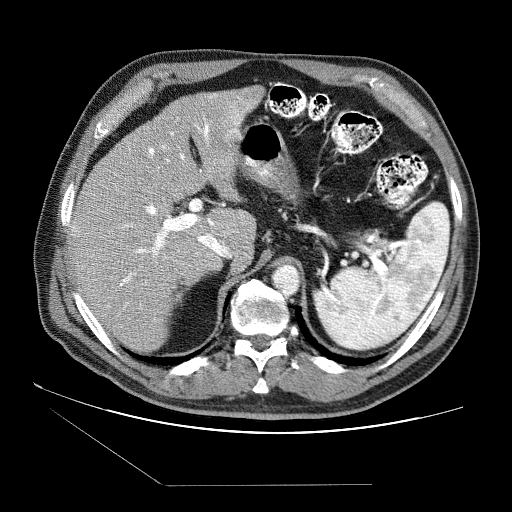
Contrast-enhanced abdominal CT (liver protocol), one axial slice; slice 53 of 87 in the series (ordered by position); reconstruction kernel STANDARD; 120 kVp; soft-tissue window (W 400 / L 40 HU); 2.5 mm slice thickness; 512 × 512 image matrix. Case-level facts recorded for this patient, not image findings: diagnosis: hepatocellular carcinoma (patient treated with transarterial chemoembolisation; whether this scan precedes or follows treatment is not stated here); TNM stage (as recorded): Stage-II; Child-Pugh class: B; tumour differentiation: no biopsy.
Structures marked on this image (semi-automatic segmentation, software-assisted and operator-edited):
- liver parenchyma outside the tumour (the mass and vessels are separate outlines, so this box may not span the whole liver): bounding box <72,86,264,352> (left, top, right, bottom; pixels)
- mass: <69,222,87,239>
- liver vessels: <92,94,250,308>